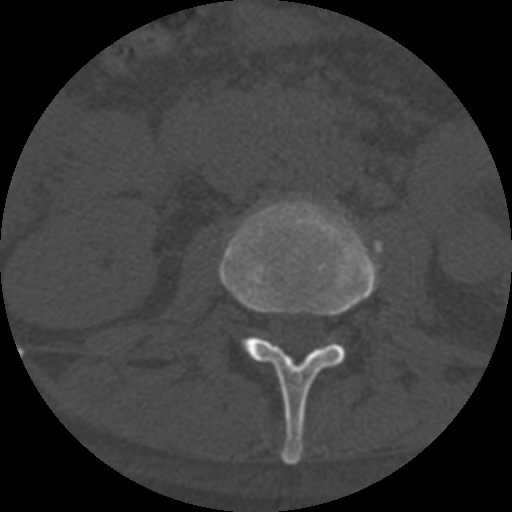
CT including the spine, one axial slice. Slice 254 of 708 in the series (ordered by position). Reconstruction kernel STANDARD. 120 kVp. One of 3 acquisitions stored at this slice position. Bone window (W 1800 / L 400 HU). 1.25 mm slice thickness. 512 × 512 image matrix, field of view 160 × 160 mm. Patient age 55 years. Case-level facts recorded for this patient, not image findings: primary cancer: colon; vertebrae with lytic lesions (as recorded): T12, L1, L5.
Annotated regions visible in this slice (semi-automatically segmented with operator editing):
- L2 vertebra: bounding box (x1, y1, x2, y2) in pixels: (219, 199, 383, 465)